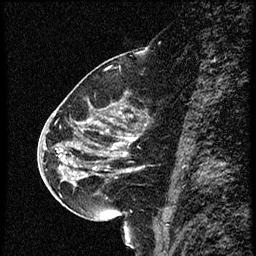
Breast MRI (dynamic contrast-enhanced), one sagittal slice. Slice 28 of 56 in the series (ordered by position). Dynamic contrast-enhanced study with each time point stored as its own series, time point 2 of 4 at this slice position (early post-contrast, ordered by acquisition time). 1.5 T. TE 4.2 ms, TR 18.9 ms. 256 × 256 image matrix, field of view 200 × 200 mm. Female patient. From the clinical record (not read from this slice): setting: breast cancer imaged before/during neoadjuvant chemotherapy; receptor status: HER2-positive.
Structures marked on this image (semi-automatic segmentation, software-assisted and operator-edited):
- analysis volume of interest (the breast-tissue region the enhancement analysis was run in; not a lesion): bounding box [x1, y1, x2, y2] px = [63, 80, 165, 215]
- tumour enhancement mask (voxels above the 100 % enhancement threshold inside the analysis volume of interest): [64, 138, 138, 183]